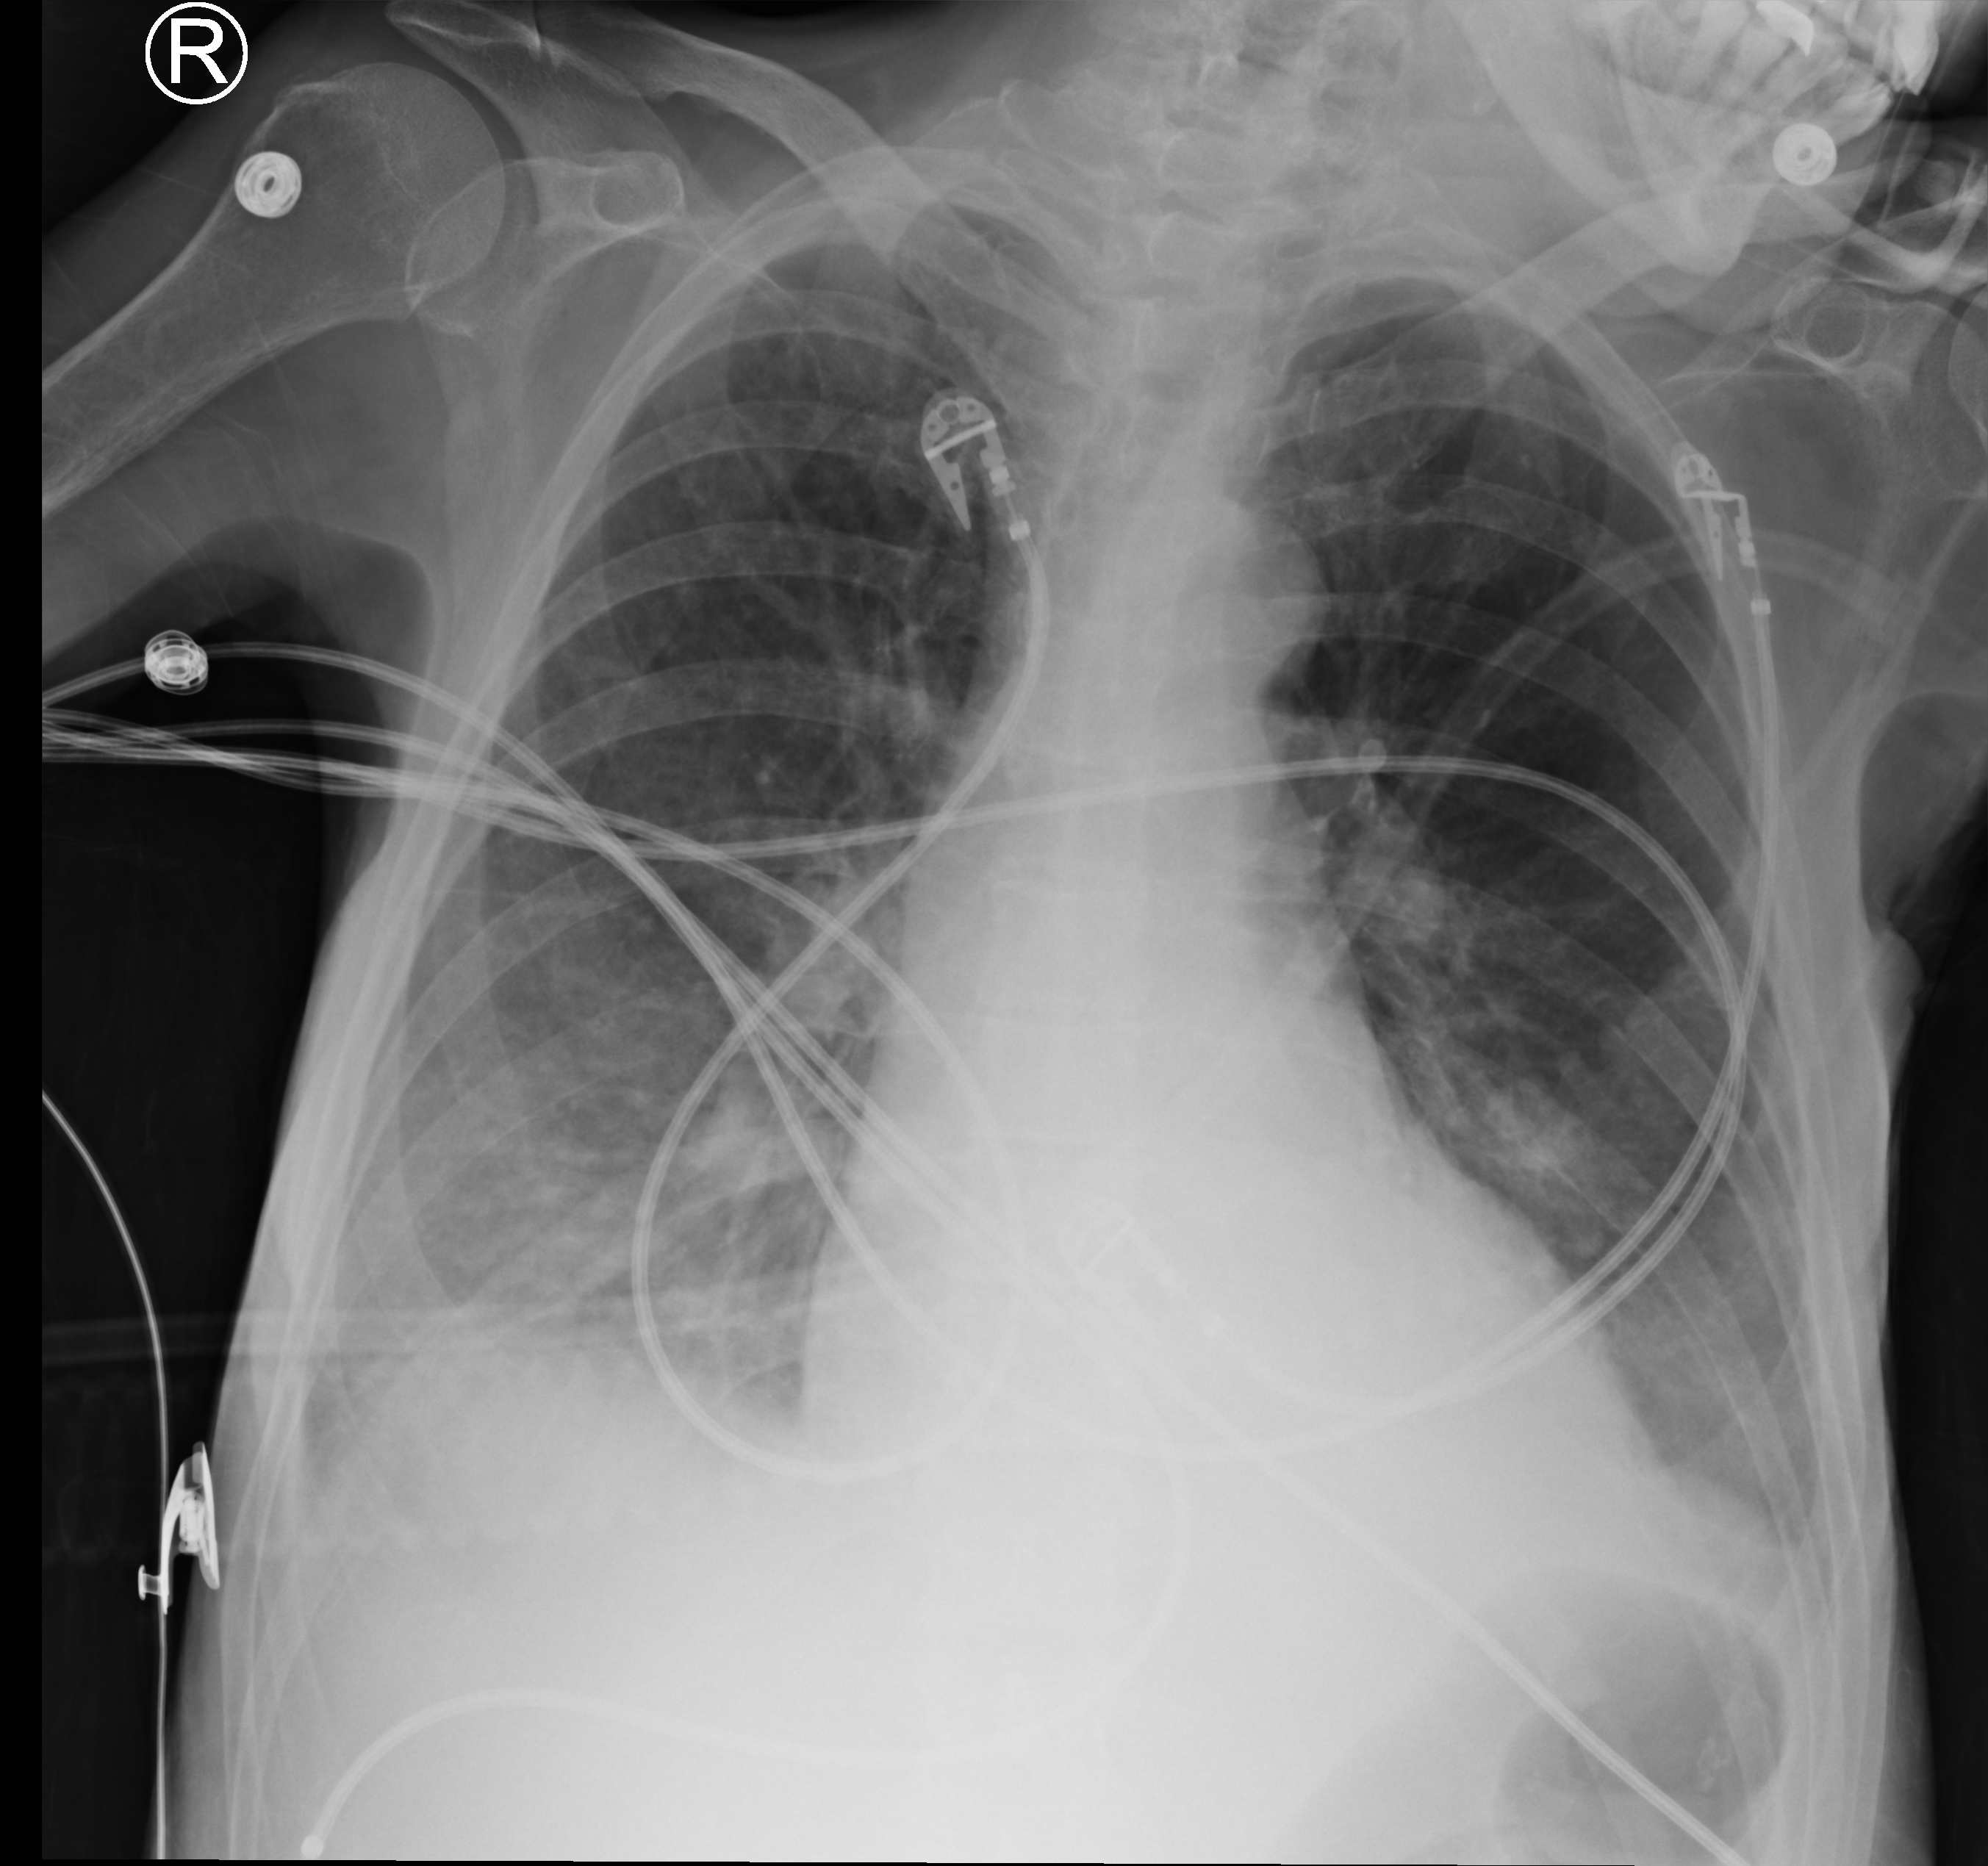
Bedside chest radiograph (computed radiography), anteroposterior (AP) projection. Female patient hospitalised with COVID-19, age 60–74 years.
From the hospital-stay record, not from the radiograph (when in the stay this image was taken is not recorded):
- admitted to intensive care during this hospital stay: yes
- length of hospital stay: 38 days